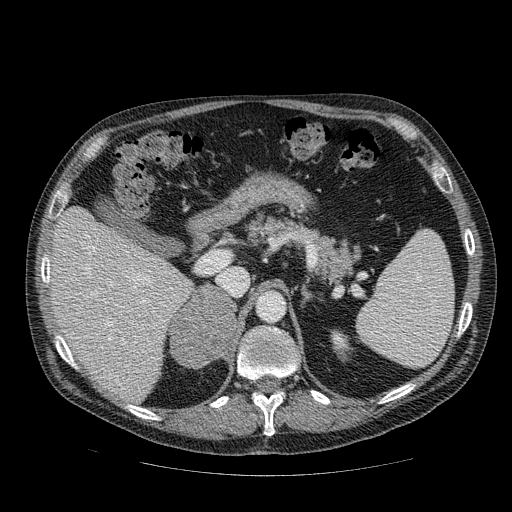
Contrast-enhanced abdominal CT, one axial slice. Position 59 of 111 along the scan axis. Reconstruction kernel STANDARD. 120 kVp. Soft-tissue window (W 400 / L 40 HU). 512 × 512 image matrix, field of view 420 × 420 mm. Male patient, age 56 years. Case-level facts recorded for this patient, not image findings: diagnosis: adrenocortical carcinoma; tumour side: right adrenal; tumour size at pathology: 9 cm; Ki-67 index: 48 %; stage (as recorded): 4.
Annotated regions visible in this slice (semi-automatic segmentation, software-assisted and operator-edited):
- mass: bounding box [x1, y1, x2, y2] px = [171, 286, 234, 367]